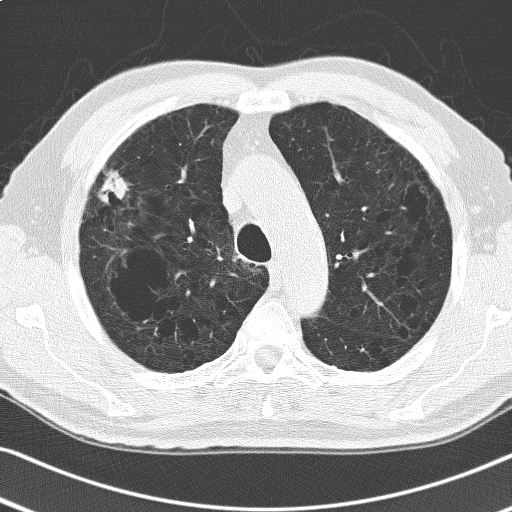
Low-dose screening chest CT, one axial slice. Position 129 of 168 along the scan axis. 120 kVp. Lung window (W 1500 / L -600 HU). 3.2 mm slice thickness. 512 × 512 image matrix, field of view 336 × 336 mm.
Annotated regions visible in this slice (expert manual segmentation):
- lesion 1 (tumor, upper lobe of right lung): bounding box <98,170,129,204> (left, top, right, bottom; pixels)